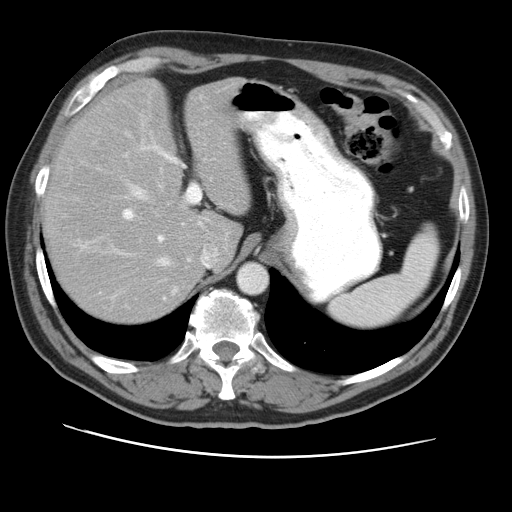
Contrast-enhanced abdominal CT, one axial slice; slice 35 of 49 in the series (ordered by position); reconstruction kernel STANDARD; 120 kVp; intravenous contrast given; soft-tissue window (W 400 / L 40 HU); 5 mm slice thickness; 512 × 512 image matrix, field of view 374 × 374 mm. Male patient, age 59 years. Case-level facts recorded for this patient, not image findings: diagnosis: colorectal cancer liver metastases, imaged before liver resection; multiple liver metastases: yes; largest metastasis: 6.3 cm; disease in both lobes: yes.
Annotated regions visible in this slice (manually delineated by an expert):
- hepatic veins: bounding box (x1, y1, x2, y2) in pixels: (132, 140, 216, 268)
- liver: (45, 79, 249, 320)
- planned liver remnant (the part of the liver to remain after resection): (45, 79, 249, 320)
- portal vein (with intrahepatic branches): (122, 149, 201, 242)